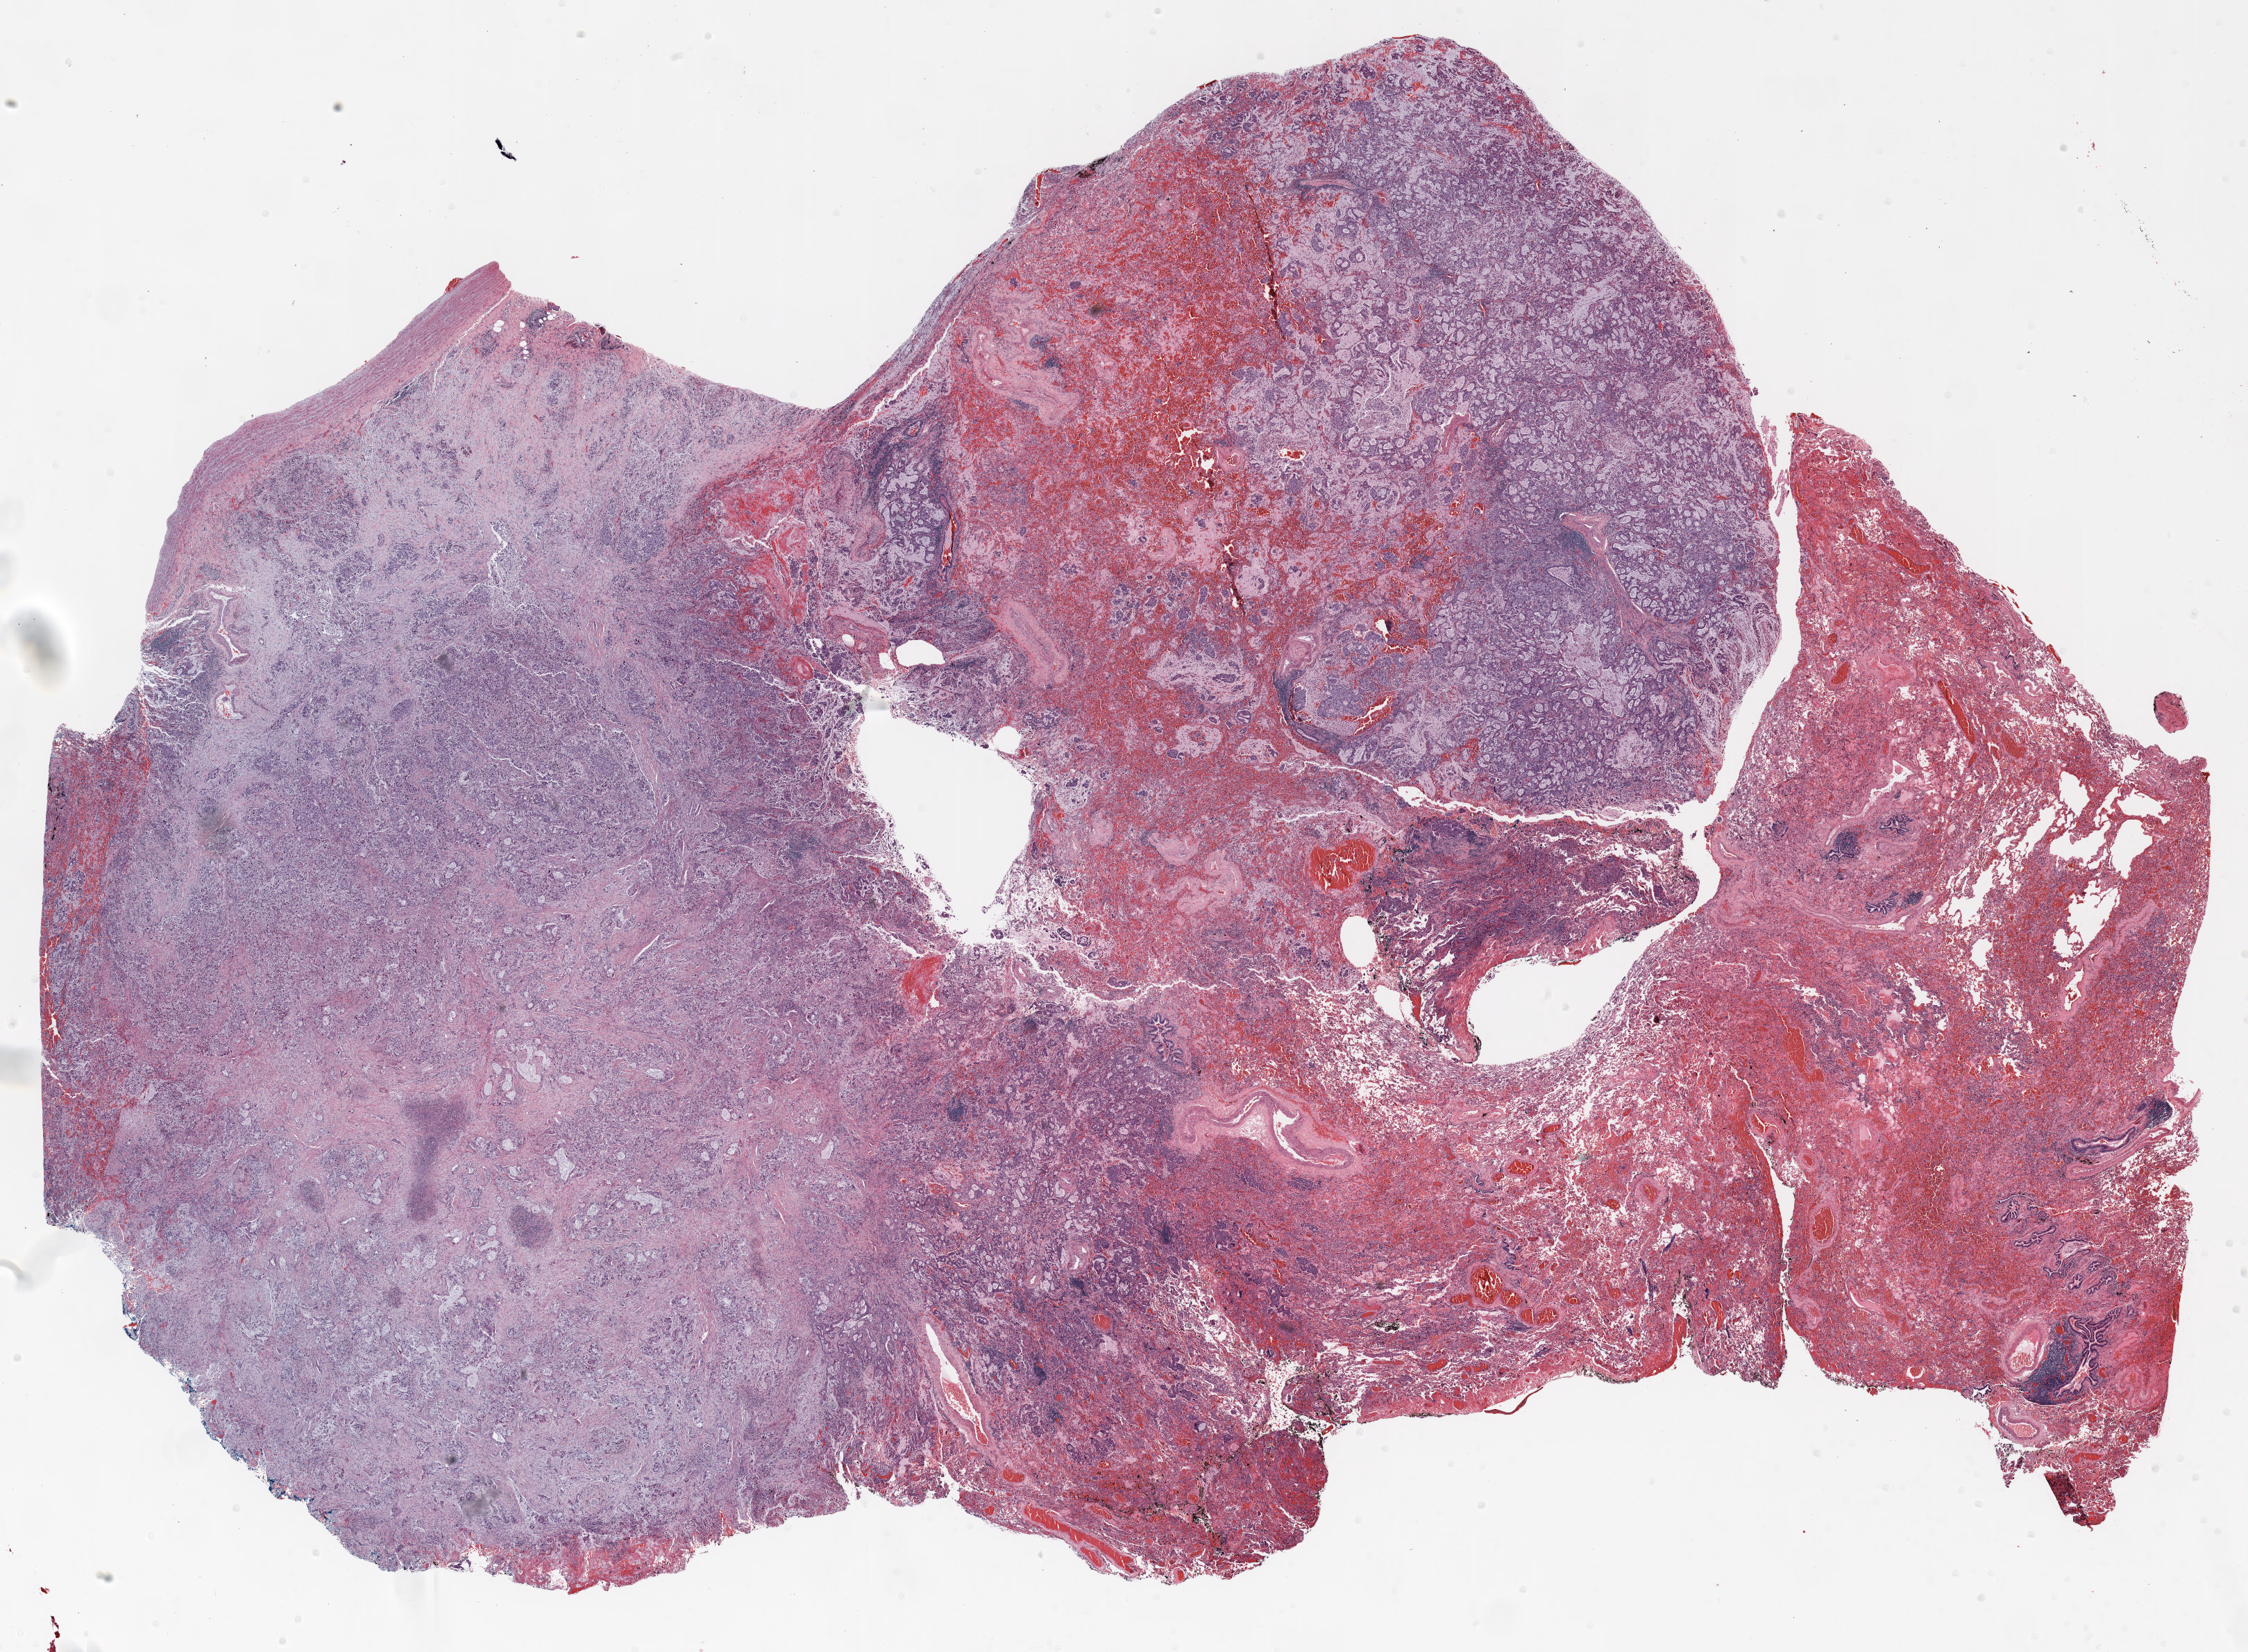
Whole-slide histology image, Hematoxylin and eosin (H&E) stained, a low-resolution overview of the entire scanned area, about 26.0 x 19.1 mm (slide scanned at 20x); FFPE section; lung tissue. Male patient, aged 59 at enrolment. Grade: poorly differentiated (G3).
Tumour size (pathology): 21 mm. Participant's lung-cancer diagnosis: Signet ring cell carcinoma (ICD-O-3 8490/3). Primary tumour location (clinical record): left lower lobe. Stage (AJCC 6th edition): IIIA.